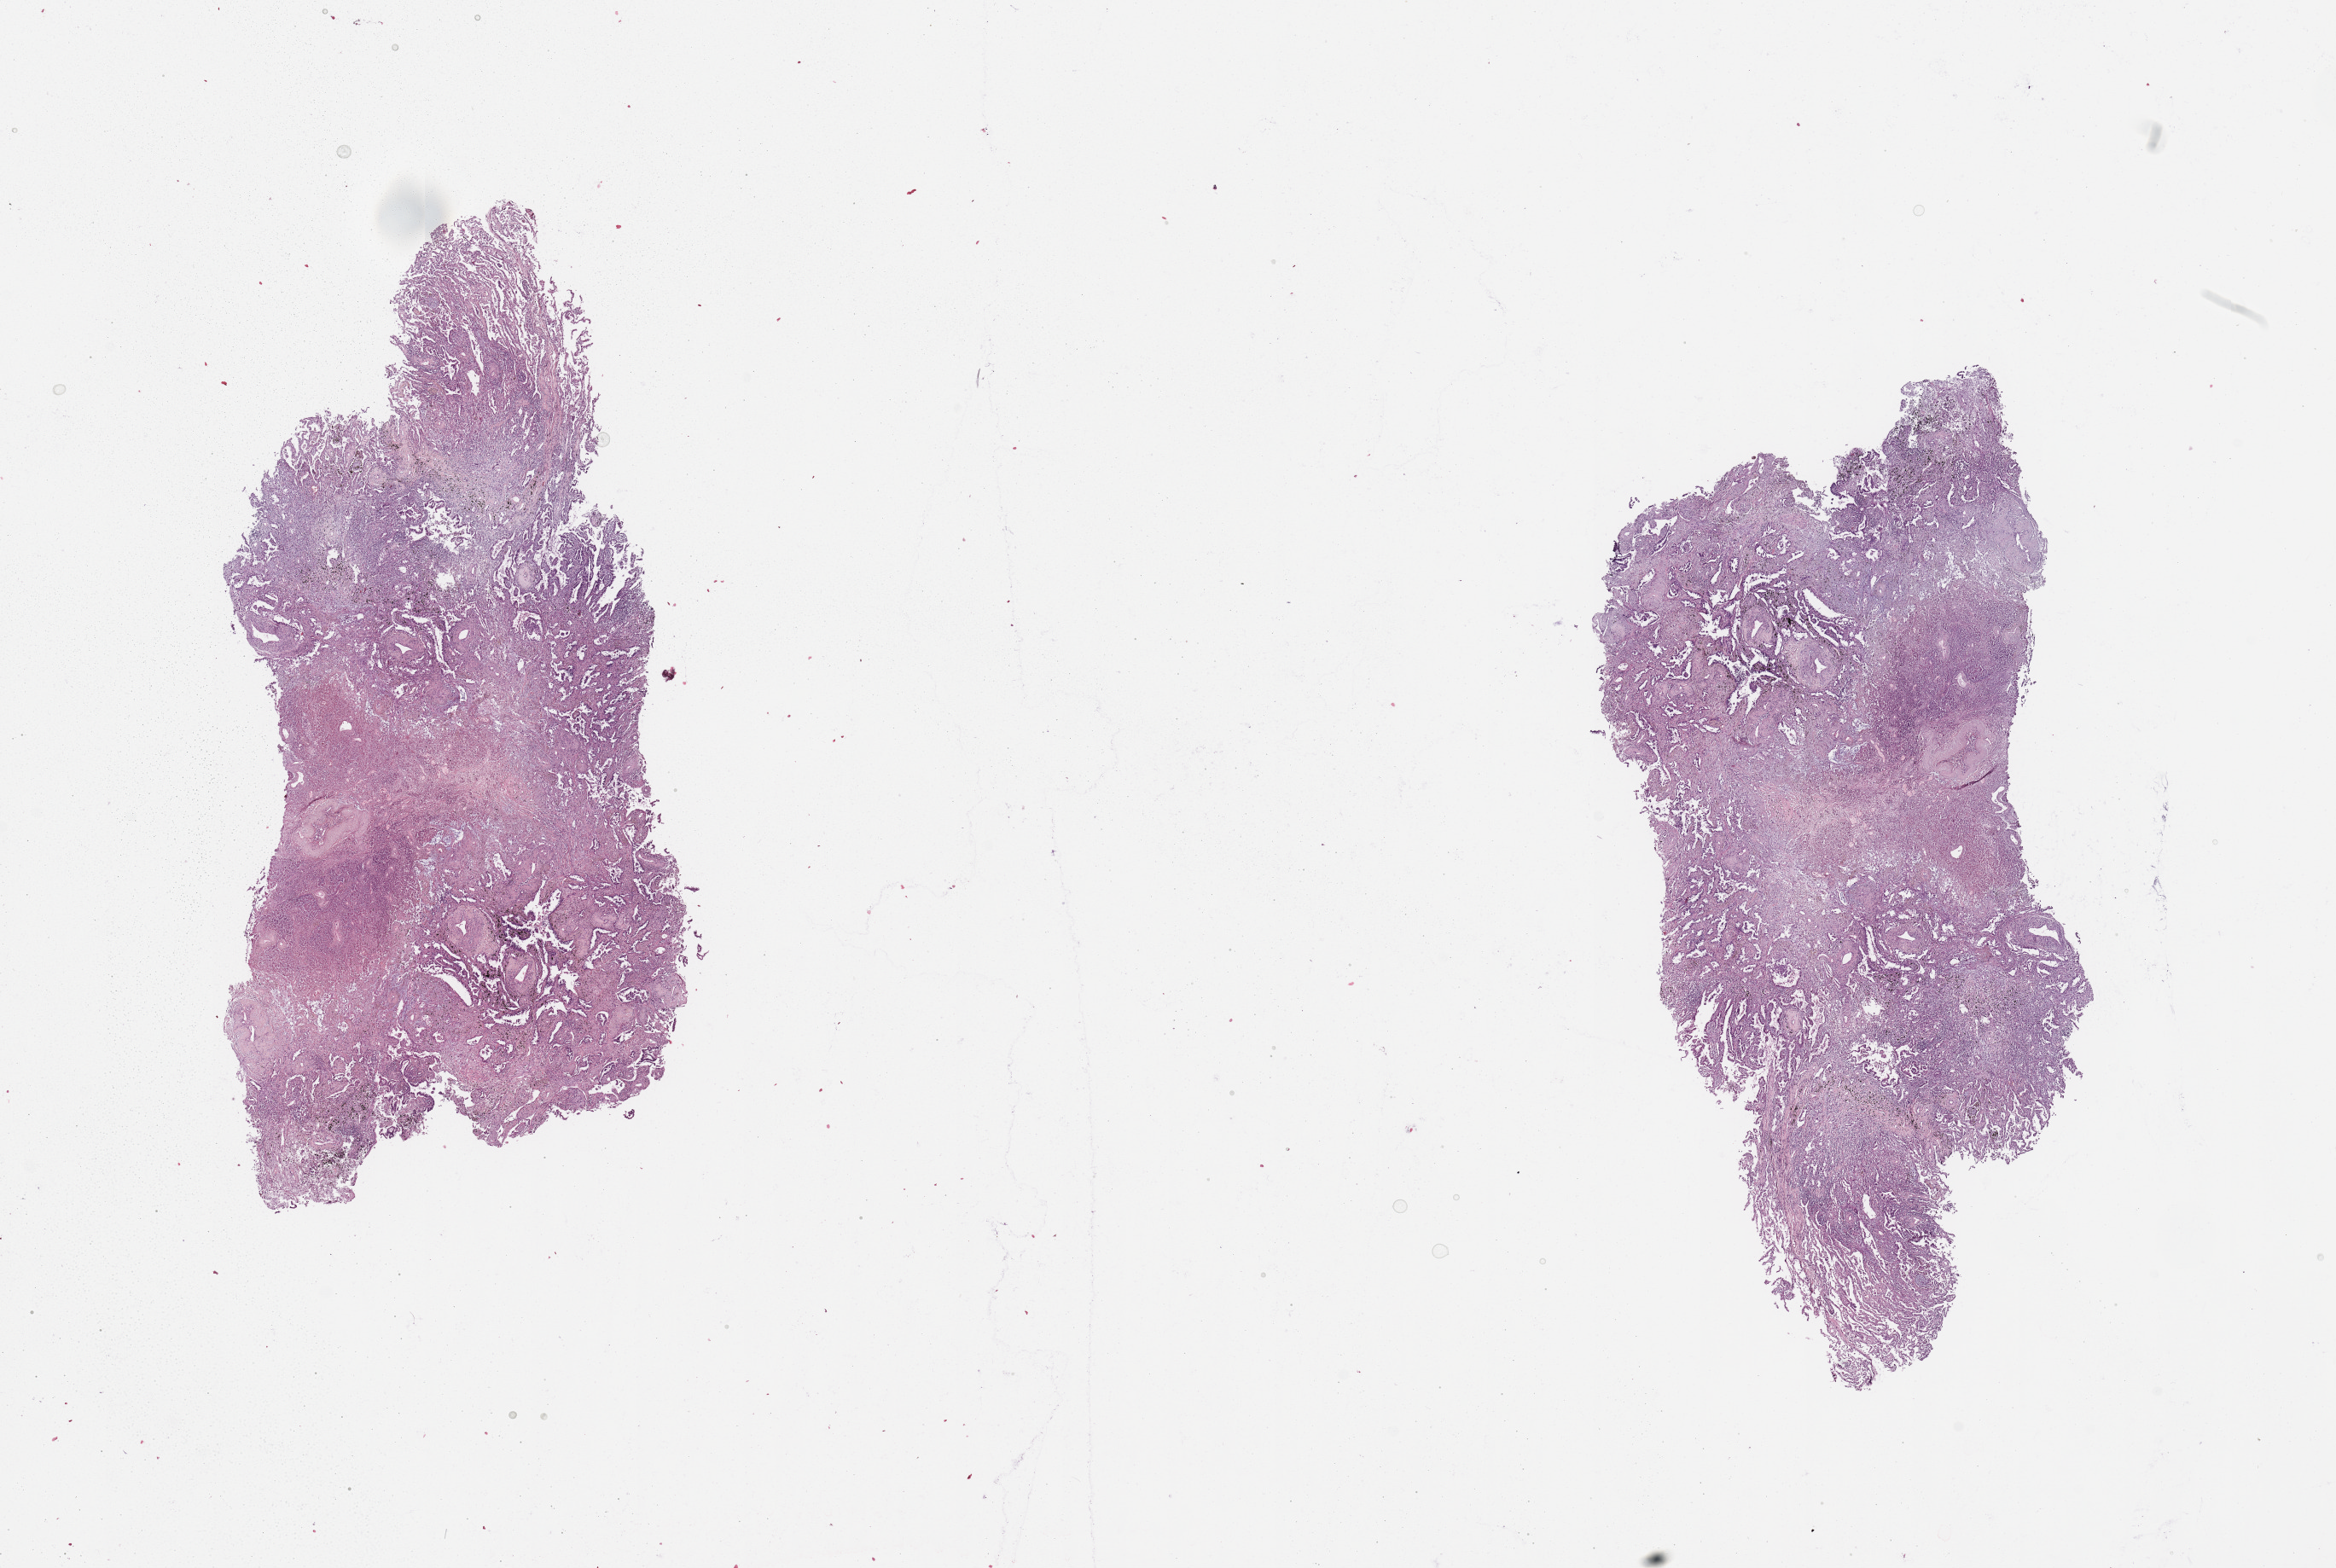
H&E-stained whole-slide image, a low-resolution overview of the entire scanned area, about 21.7 x 14.5 mm; tumour tissue sample, lung. 68-year-old male patient.
Histologic diagnosis: Adenocarcinoma, NOS.